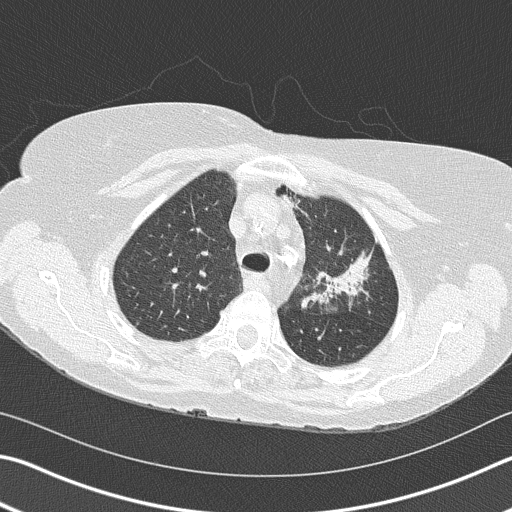
Low-dose screening chest CT, axial slice; second screening round (one year after baseline); lung window (W 1500 / L -600 HU); 2 mm slice thickness; lung (sharp) reconstruction kernel (B50f). Female, age 68 years at enrolment.
Lesion marked by an expert reader, bounding box <292,219,382,319> (left, top, right, bottom; pixels). The exam's reader record, not a measurement of the box and not confirmed to be the same lesion: non-calcified nodule or mass ≥4 mm, left upper lobe, 4 × 2 mm, spiculated (stellate) margins, soft tissue attenuation, pre-existing on the prior screen: yes; interval growth: yes. Official screen result: positive, other. Participant outcome: lung cancer diagnosed 392 days after this screen — adenocarcinoma, NOS, left upper lobe, poorly differentiated (G3), stage IB (AJCC 6th edition), 50 mm at pathology.